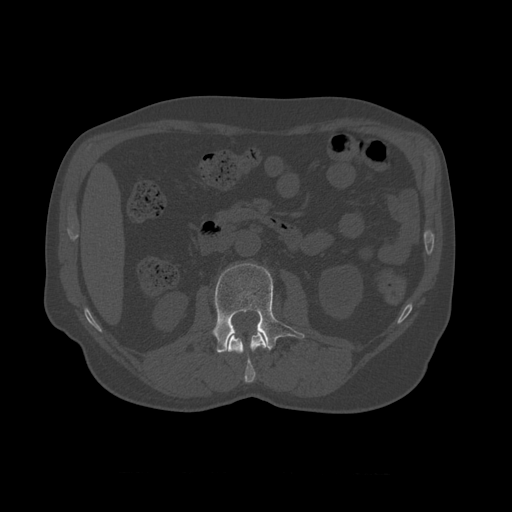
CT including the spine, one axial slice. Position 336 of 450 along the scan axis. Reconstruction kernel STANDARD. 120 kVp. Bone window (W 1800 / L 400 HU). 1.25 mm slice thickness. 512 × 512 image matrix, field of view 405 × 405 mm. Patient age 75 years. Case-level facts recorded for this patient, not image findings: primary cancer: prostate.
Outlined on this slice (semi-automatically segmented with operator editing):
- L1 vertebra: bounding box (x1, y1, x2, y2) in pixels: (227, 329, 268, 383)
- L2 vertebra: (212, 263, 305, 353)